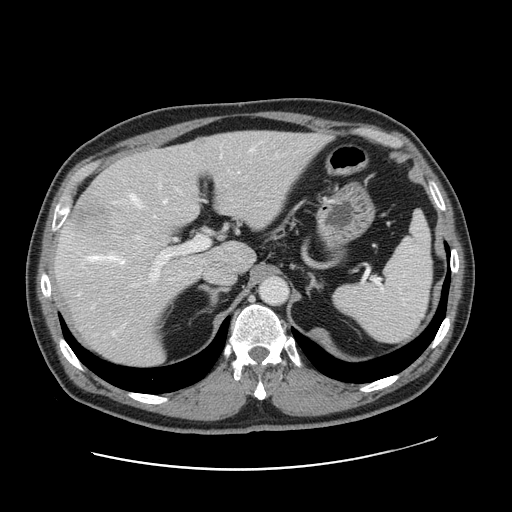
Contrast-enhanced abdominal CT, one axial slice; slice 109 of 178 in the series (ordered by position); intravenous contrast given; soft-tissue window (W 400 / L 40 HU); 512 × 512 image matrix. Male patient, age 63 years. Case-level facts recorded for this patient, not image findings: diagnosis: colorectal cancer liver metastases, imaged before liver resection; multiple liver metastases: yes; largest metastasis: 8 cm; disease in both lobes: yes.
Outlined on this slice (manually delineated by an expert):
- hepatic veins: bounding box (x1, y1, x2, y2) in pixels: (89, 148, 253, 264)
- liver: (56, 131, 323, 367)
- planned liver remnant (the part of the liver to remain after resection): (130, 131, 323, 272)
- portal vein (with intrahepatic branches): (151, 198, 211, 279)
- liver metastasis: (296, 161, 306, 174)
- liver metastasis: (70, 206, 109, 234)